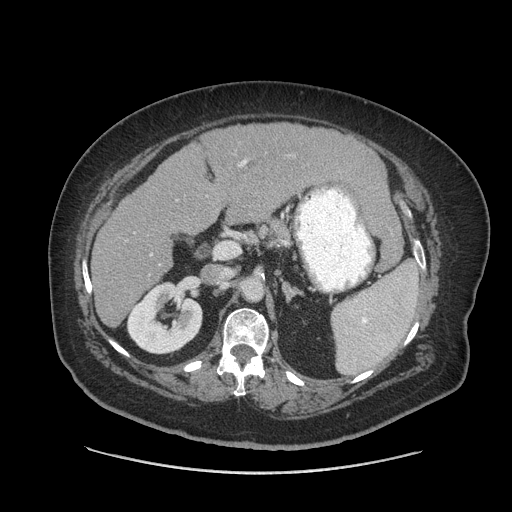
Contrast-enhanced abdominal CT (liver protocol), one axial slice; position 41 of 91 along the scan axis; reconstruction kernel STANDARD; 140 kVp; soft-tissue window (W 400 / L 40 HU); 2.5 mm slice thickness; 512 × 512 image matrix. From the clinical record (not read from this slice): diagnosis: hepatocellular carcinoma (patient treated with transarterial chemoembolisation; whether this scan precedes or follows treatment is not stated here); TNM stage (as recorded): Stage-I; Child-Pugh class: A; tumour differentiation: well differentiated; tumour nodularity: uninodular.
Annotated regions visible in this slice (semi-automatically segmented with operator editing):
- liver parenchyma outside the tumour (the mass and vessels are separate outlines, so this box may not span the whole liver): bounding box [x1, y1, x2, y2] px = [90, 122, 390, 326]
- liver vessels: [151, 160, 247, 256]